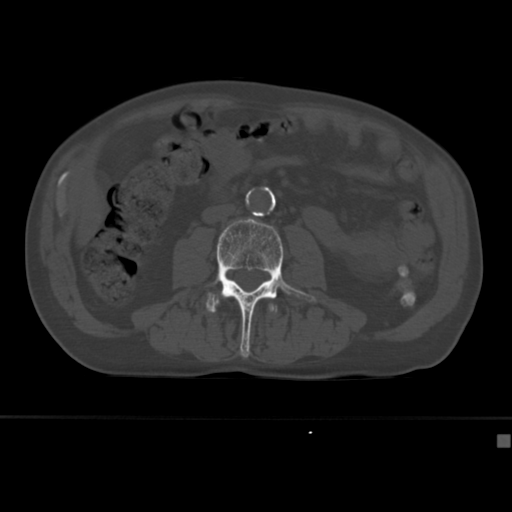
CT including the spine, one axial slice. Position 127 of 430 along the scan axis. Reconstruction kernel Br40s. Bone window (W 1800 / L 400 HU). 1.5 mm slice thickness. 512 × 512 image matrix, field of view 337 × 337 mm. Male patient, age 64 years. Case-level facts recorded for this patient, not image findings: primary cancer: uterus; vertebrae with lytic lesions (as recorded): T1, T4, T5, T7, L5.
Structures marked on this image (semi-automatic segmentation, software-assisted and operator-edited):
- L2 vertebra: bounding box [x1, y1, x2, y2] px = [267, 298, 277, 311]
- L3 vertebra: [208, 218, 317, 358]
- L4 vertebra: [206, 291, 213, 311]